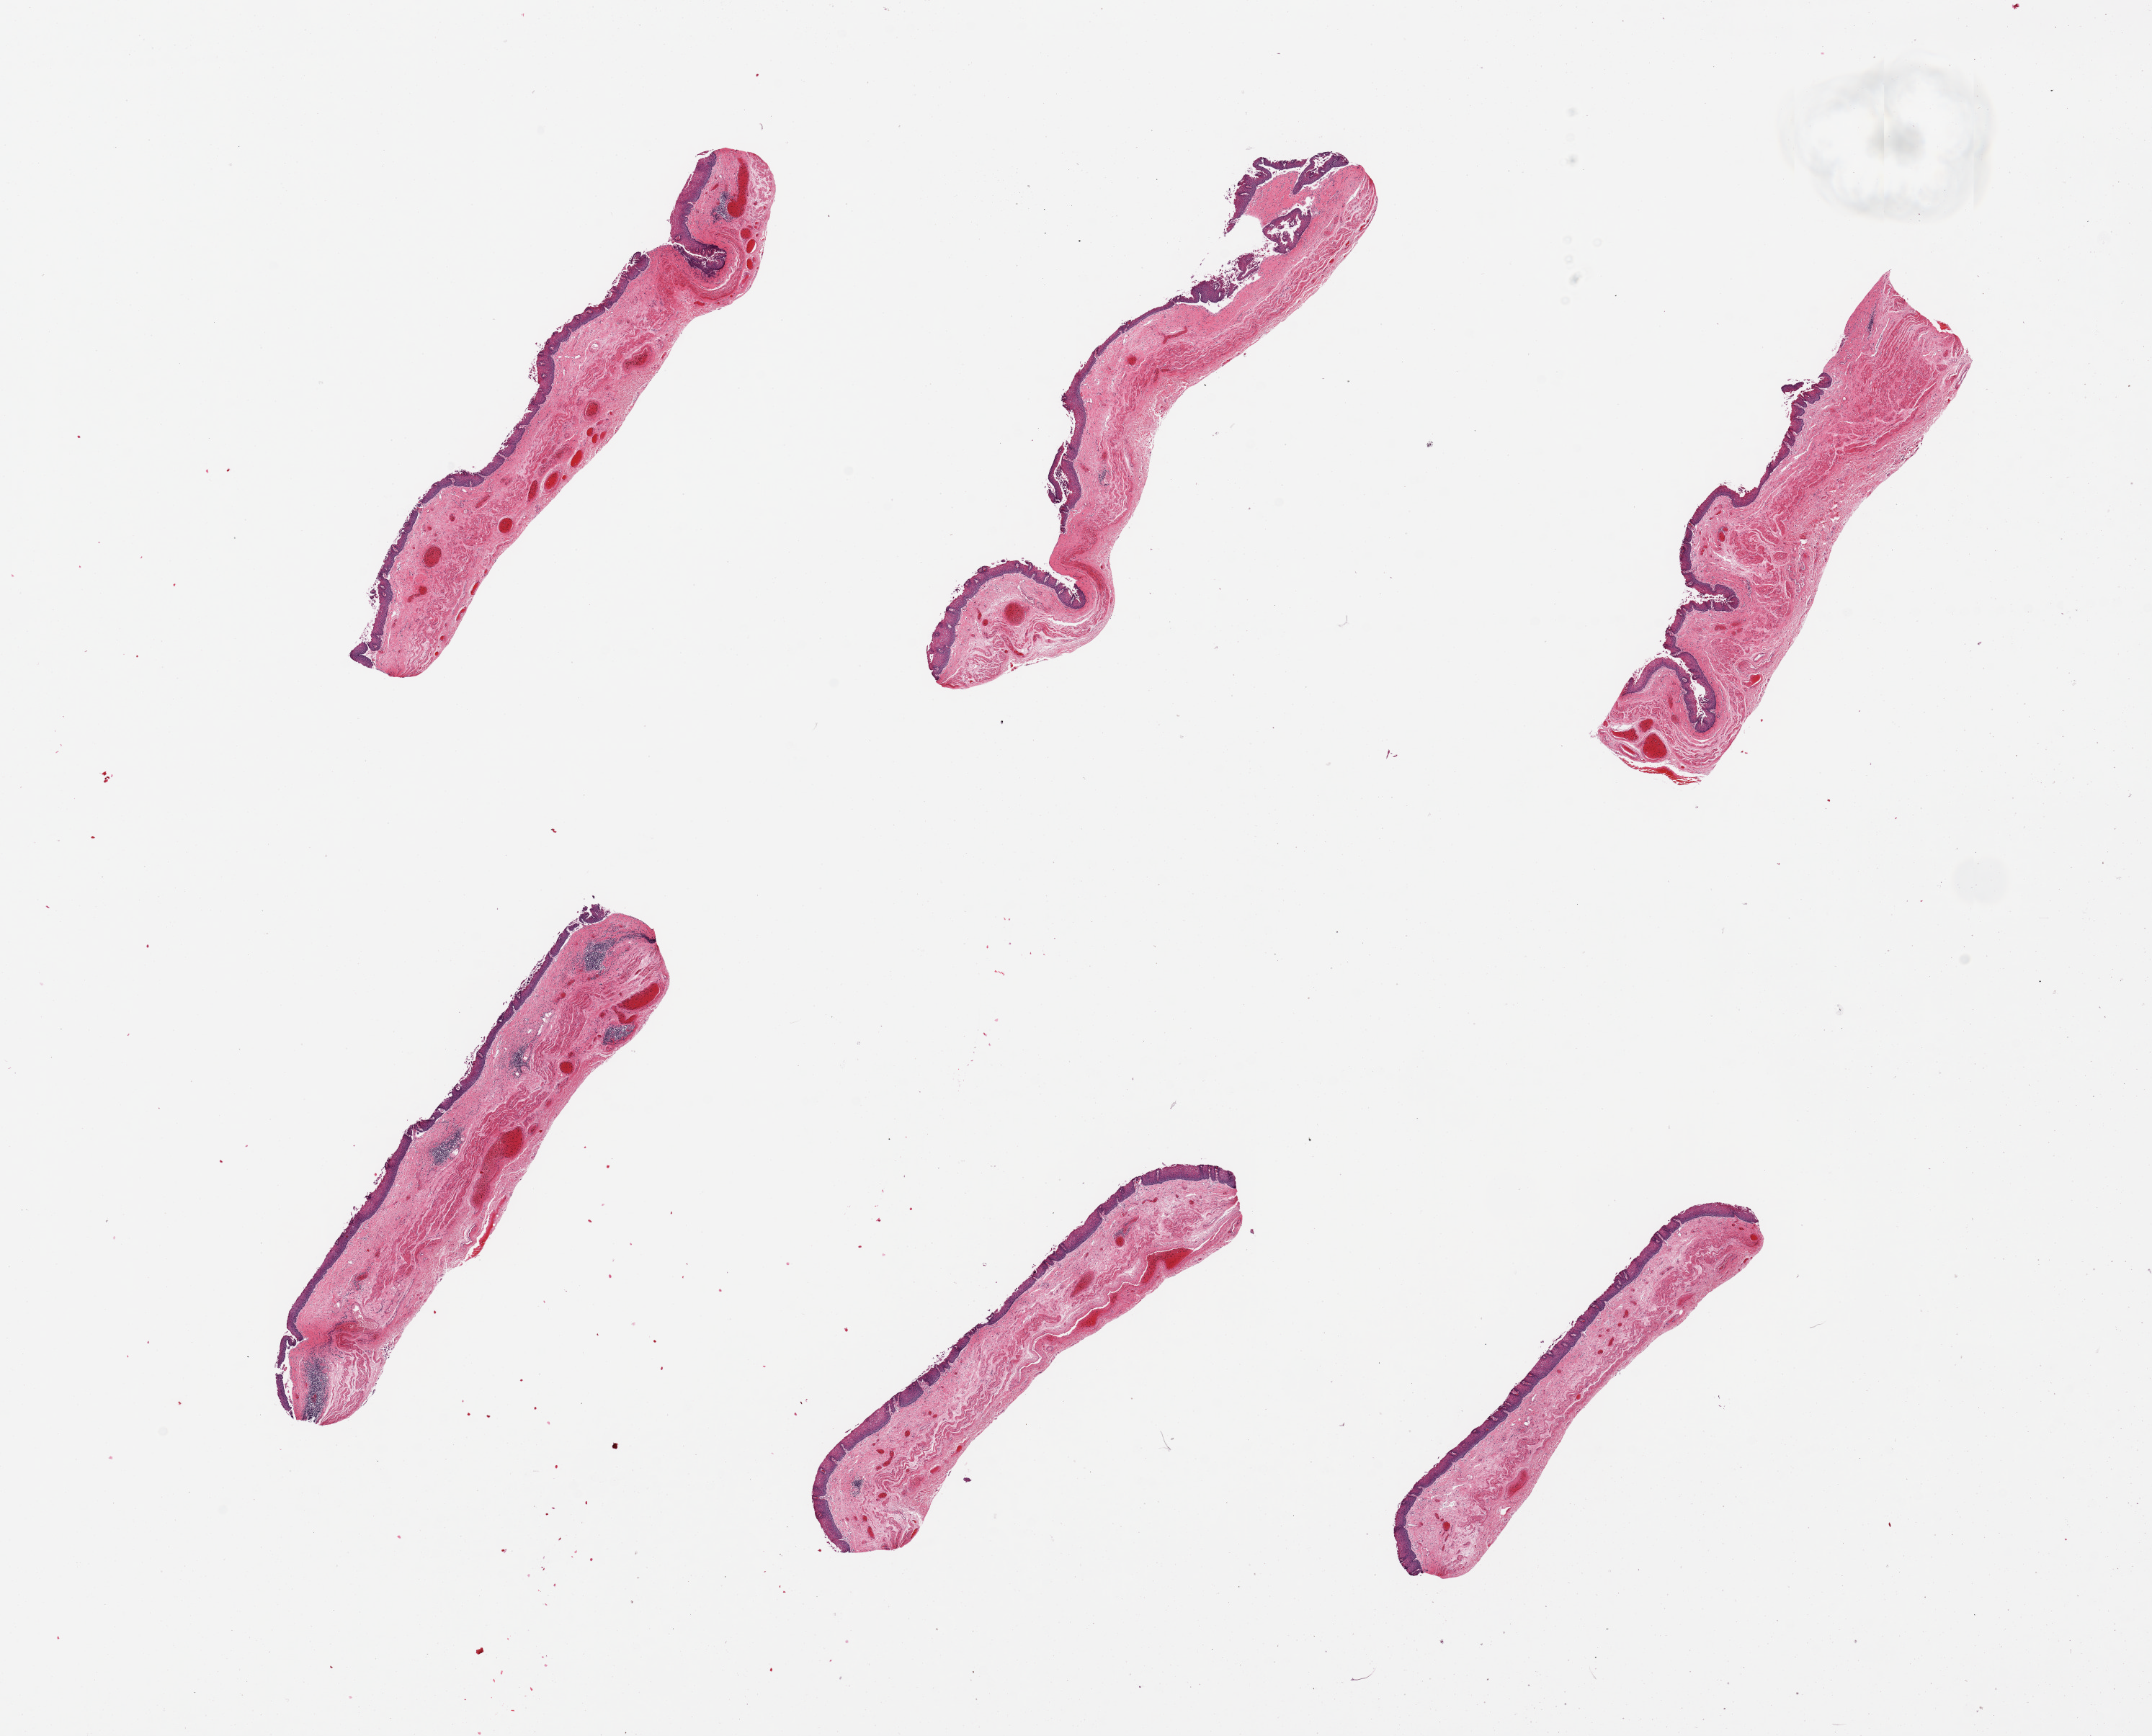
Digitized haematoxylin and eosin-stained section, brightfield — a low-resolution overview of the entire scanned area, about 23.6 x 19.1 mm, PAXgene-fixed, paraffin-embedded tissue, section of esophageal mucous membrane (target tissue), tissue donor sample. Donor sex: female.
• reviewer comment on this tissue sample: 6 pieces, squamous mucosa is ~1--15% thickness, partly sloughing